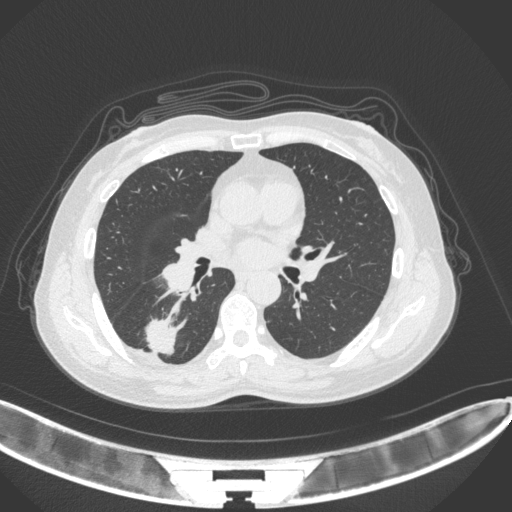
Chest CT, one axial slice; slice 161 of 352 in the series (ordered by position); reconstruction kernel B31f; lung window (W 1500 / L -600 HU); 1 mm slice thickness; 512 × 512 image matrix, field of view 400 × 400 mm. Patient: female, 55 years. Case-level facts recorded for this patient, not image findings: clinical TNM (as recorded): T1c N1 M0.
Outlined on this slice (rectangle marked by the reading radiologist):
- lung tumour (recorded histology: adenocarcinoma): bounding box <142,316,182,357> (left, top, right, bottom; pixels)